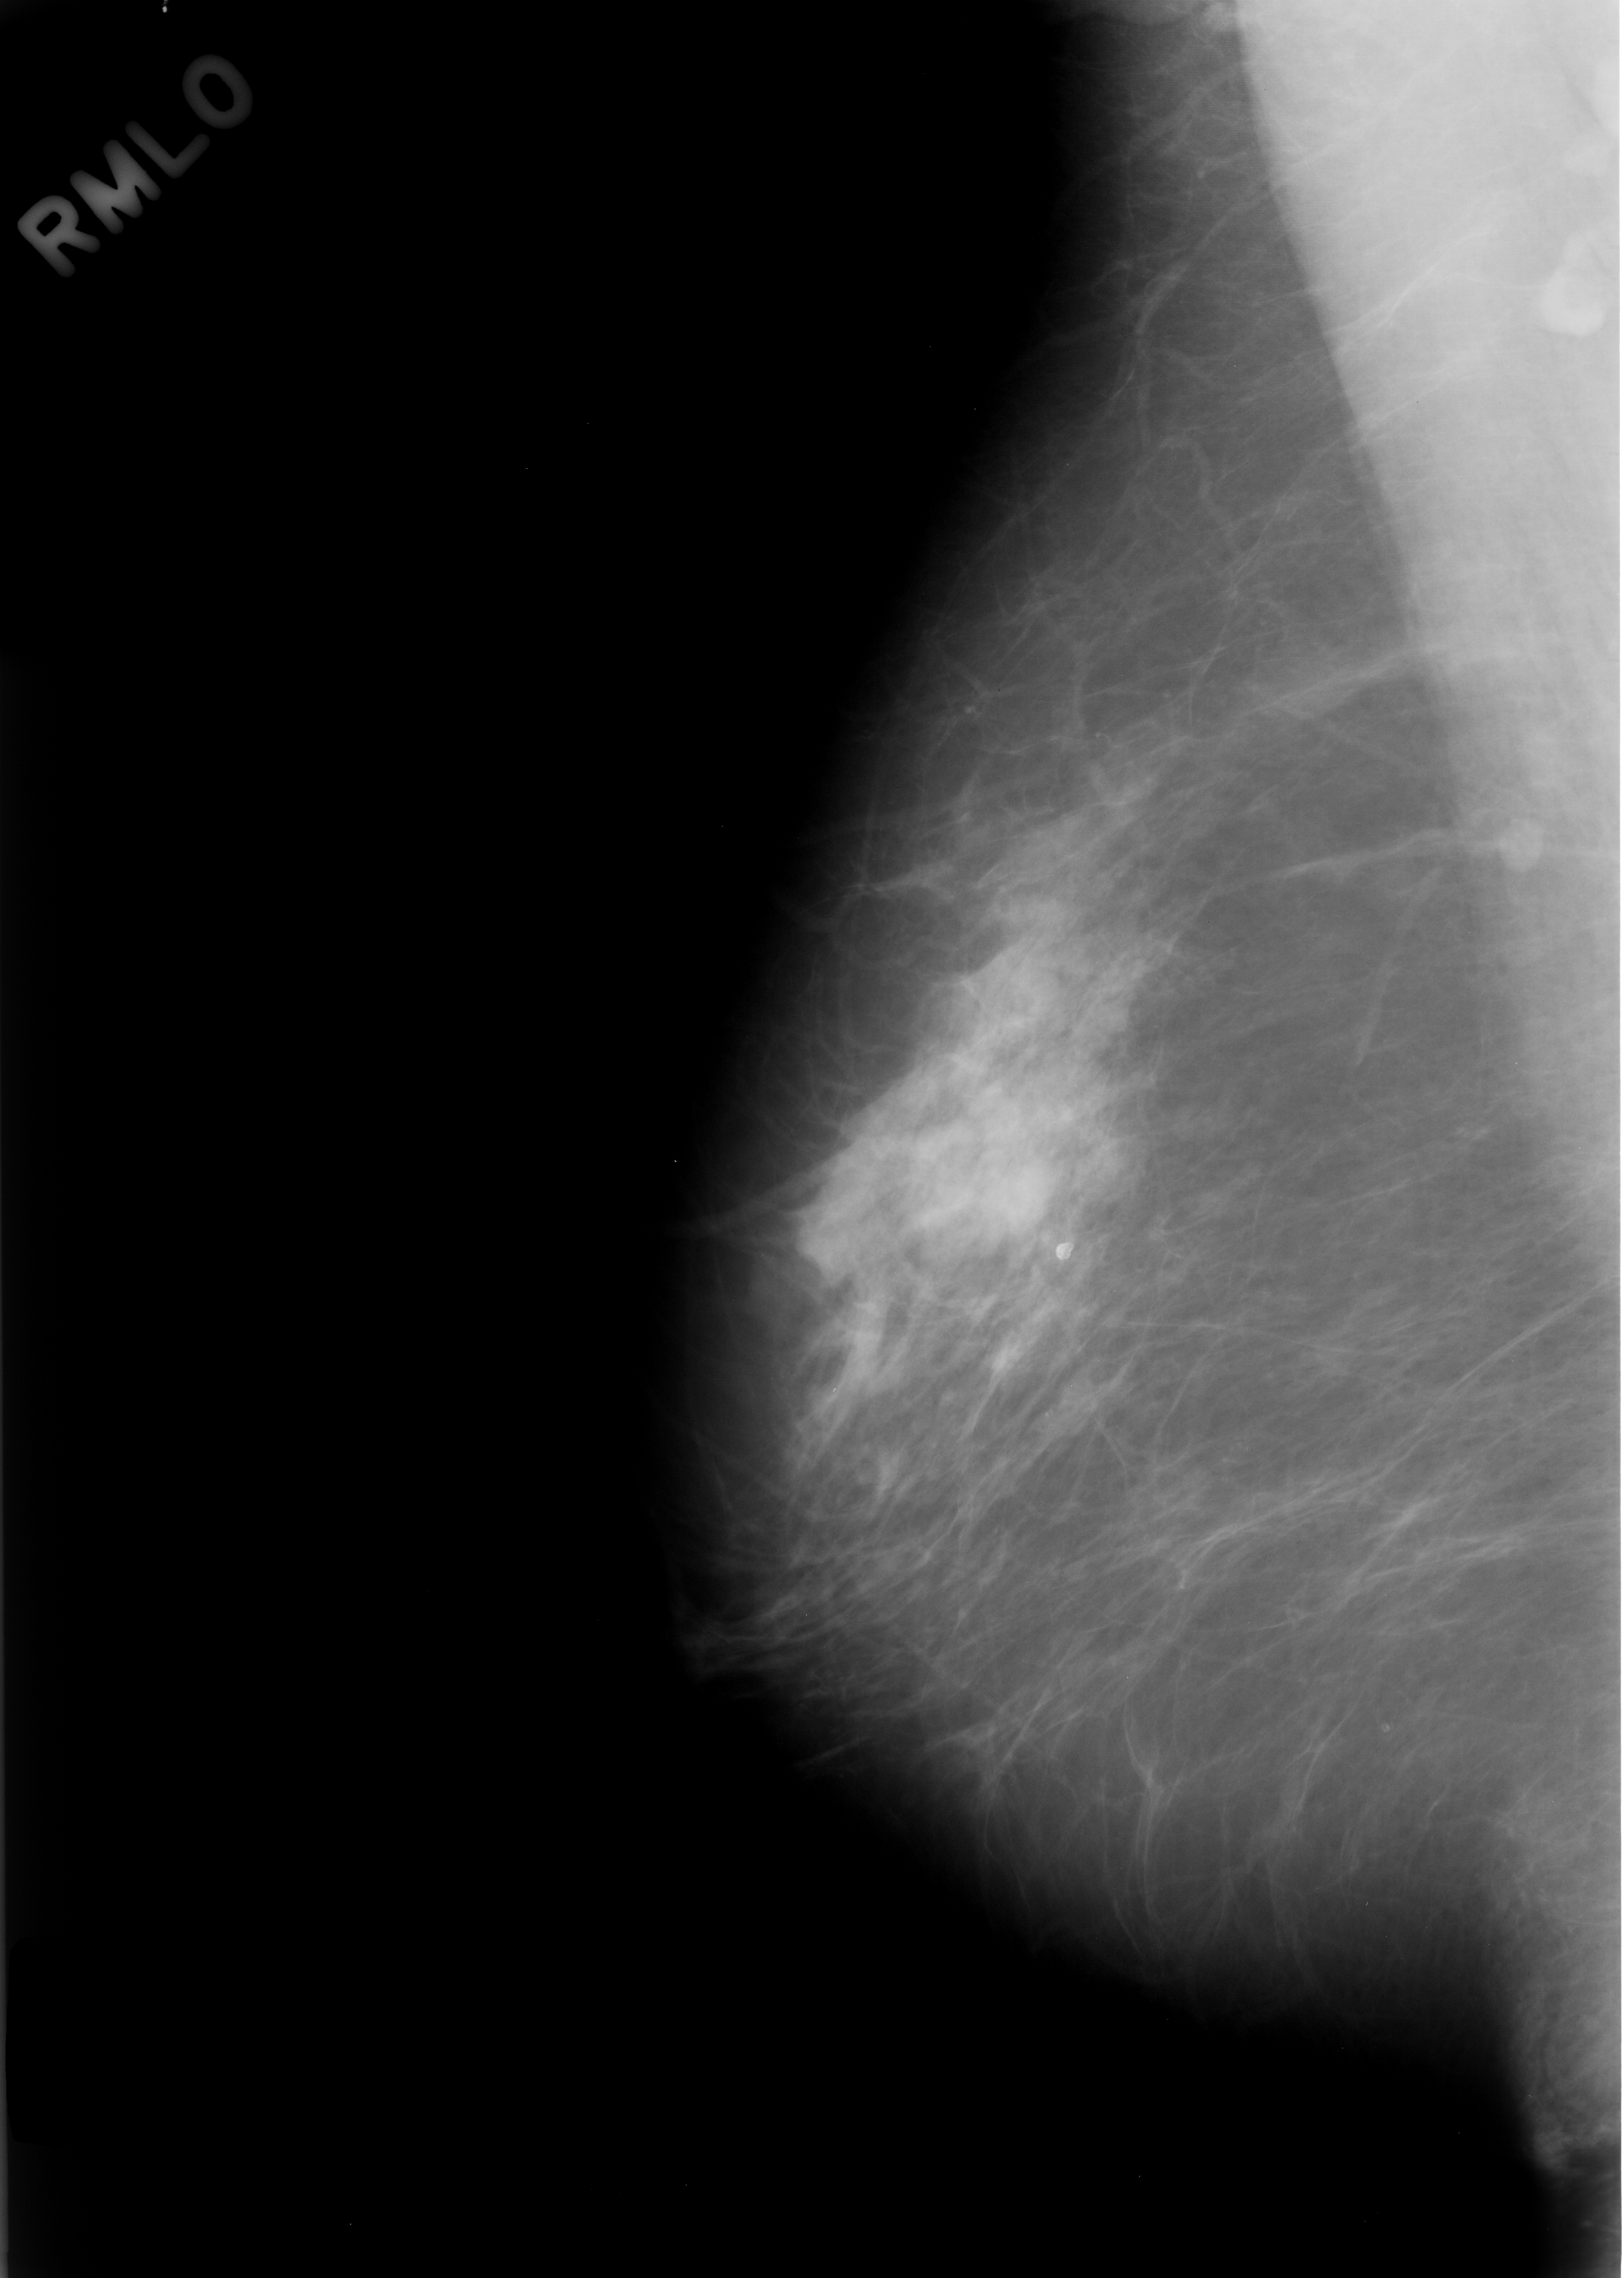
Mammogram (digitized film); right breast; mediolateral oblique (MLO) view.
Abnormality record for this image: mass, shape lobulated, margins microlobulated; BI-RADS assessment category 3; subtlety rating 5 on a 1 (subtle) to 5 (obvious) scale; benign; no additional work-up was recommended (benign without callback).